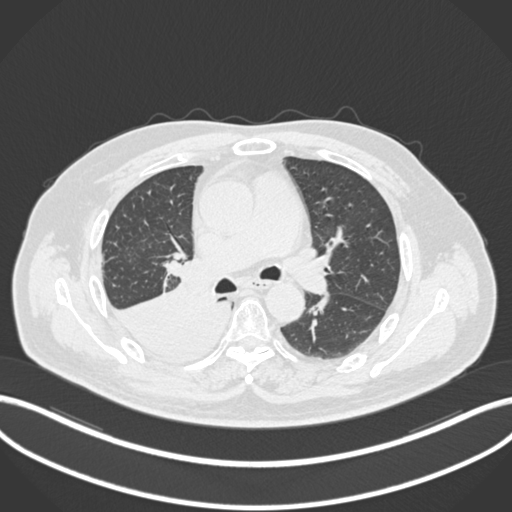
Chest CT, one axial slice. Position 116 of 218 along the scan axis. 120 kVp. Lung window (W 1500 / L -600 HU). 512 × 512 image matrix, field of view 400 × 400 mm. Patient: male, 68 years. Case-level facts recorded for this patient, not image findings: clinical TNM (as recorded): T2a N0 M0.
Outlined on this slice (rectangle marked by the reading radiologist):
- lung tumour (recorded histology: adenocarcinoma): bounding box <111,289,232,360> (left, top, right, bottom; pixels)